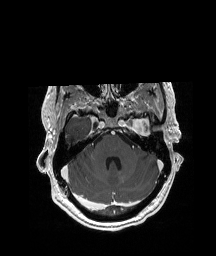
Brain MRI from a brain-tumour surgery series, one axial slice. T1-weighted post-contrast. 1 mm slice thickness. 216 × 256 image matrix. From the clinical record (not read from this slice): histopathology: Glioblastoma; WHO grade: 4; IDH mutation: no; tumour location: Left Anterior/Superior Temporal.
Annotated regions visible in this slice (expert manual segmentation):
- previous resection cavity: bounding box [x1, y1, x2, y2] px = [148, 129, 150, 131]
- tumour: [129, 113, 148, 131]